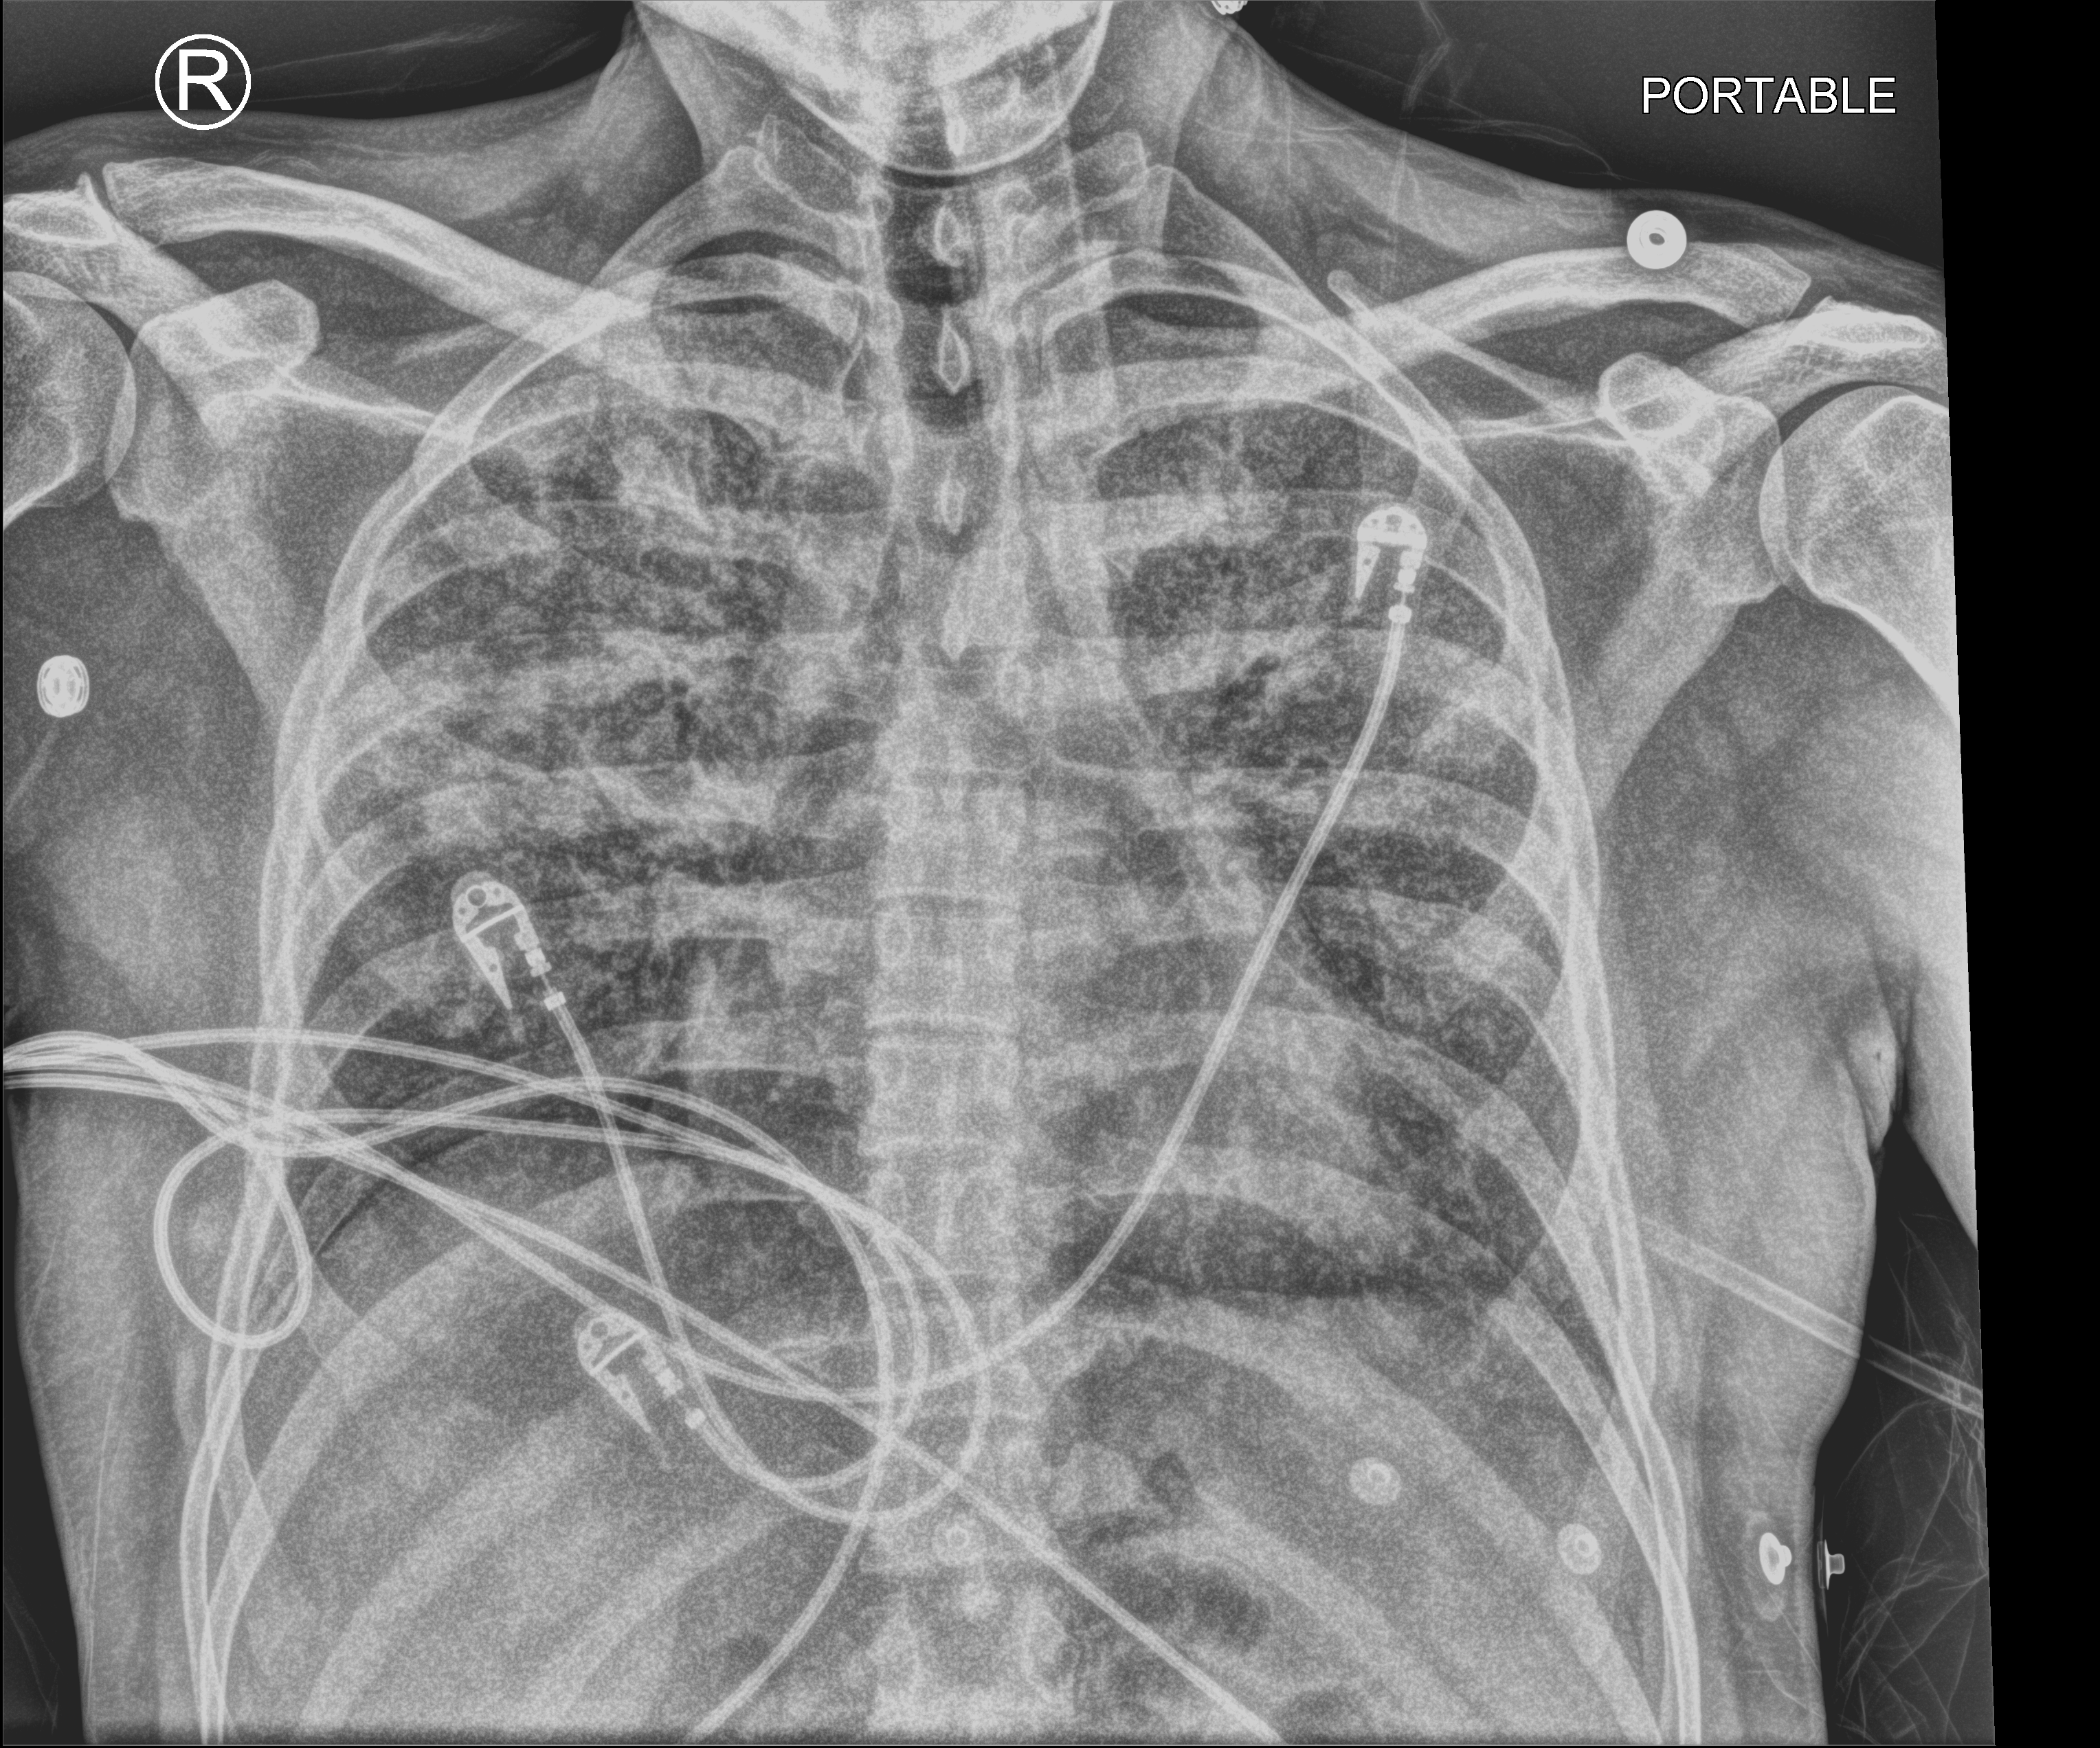
Chest X-ray (portable), anteroposterior (AP) projection. Patient hospitalised with COVID-19; male, aged 18–59 years.
Hospital-stay facts (about this admission, not read from this image; timing relative to this image not recorded): COPD (admission record): no; admitted to intensive care during this hospital stay: yes; diabetes (admission record): no.